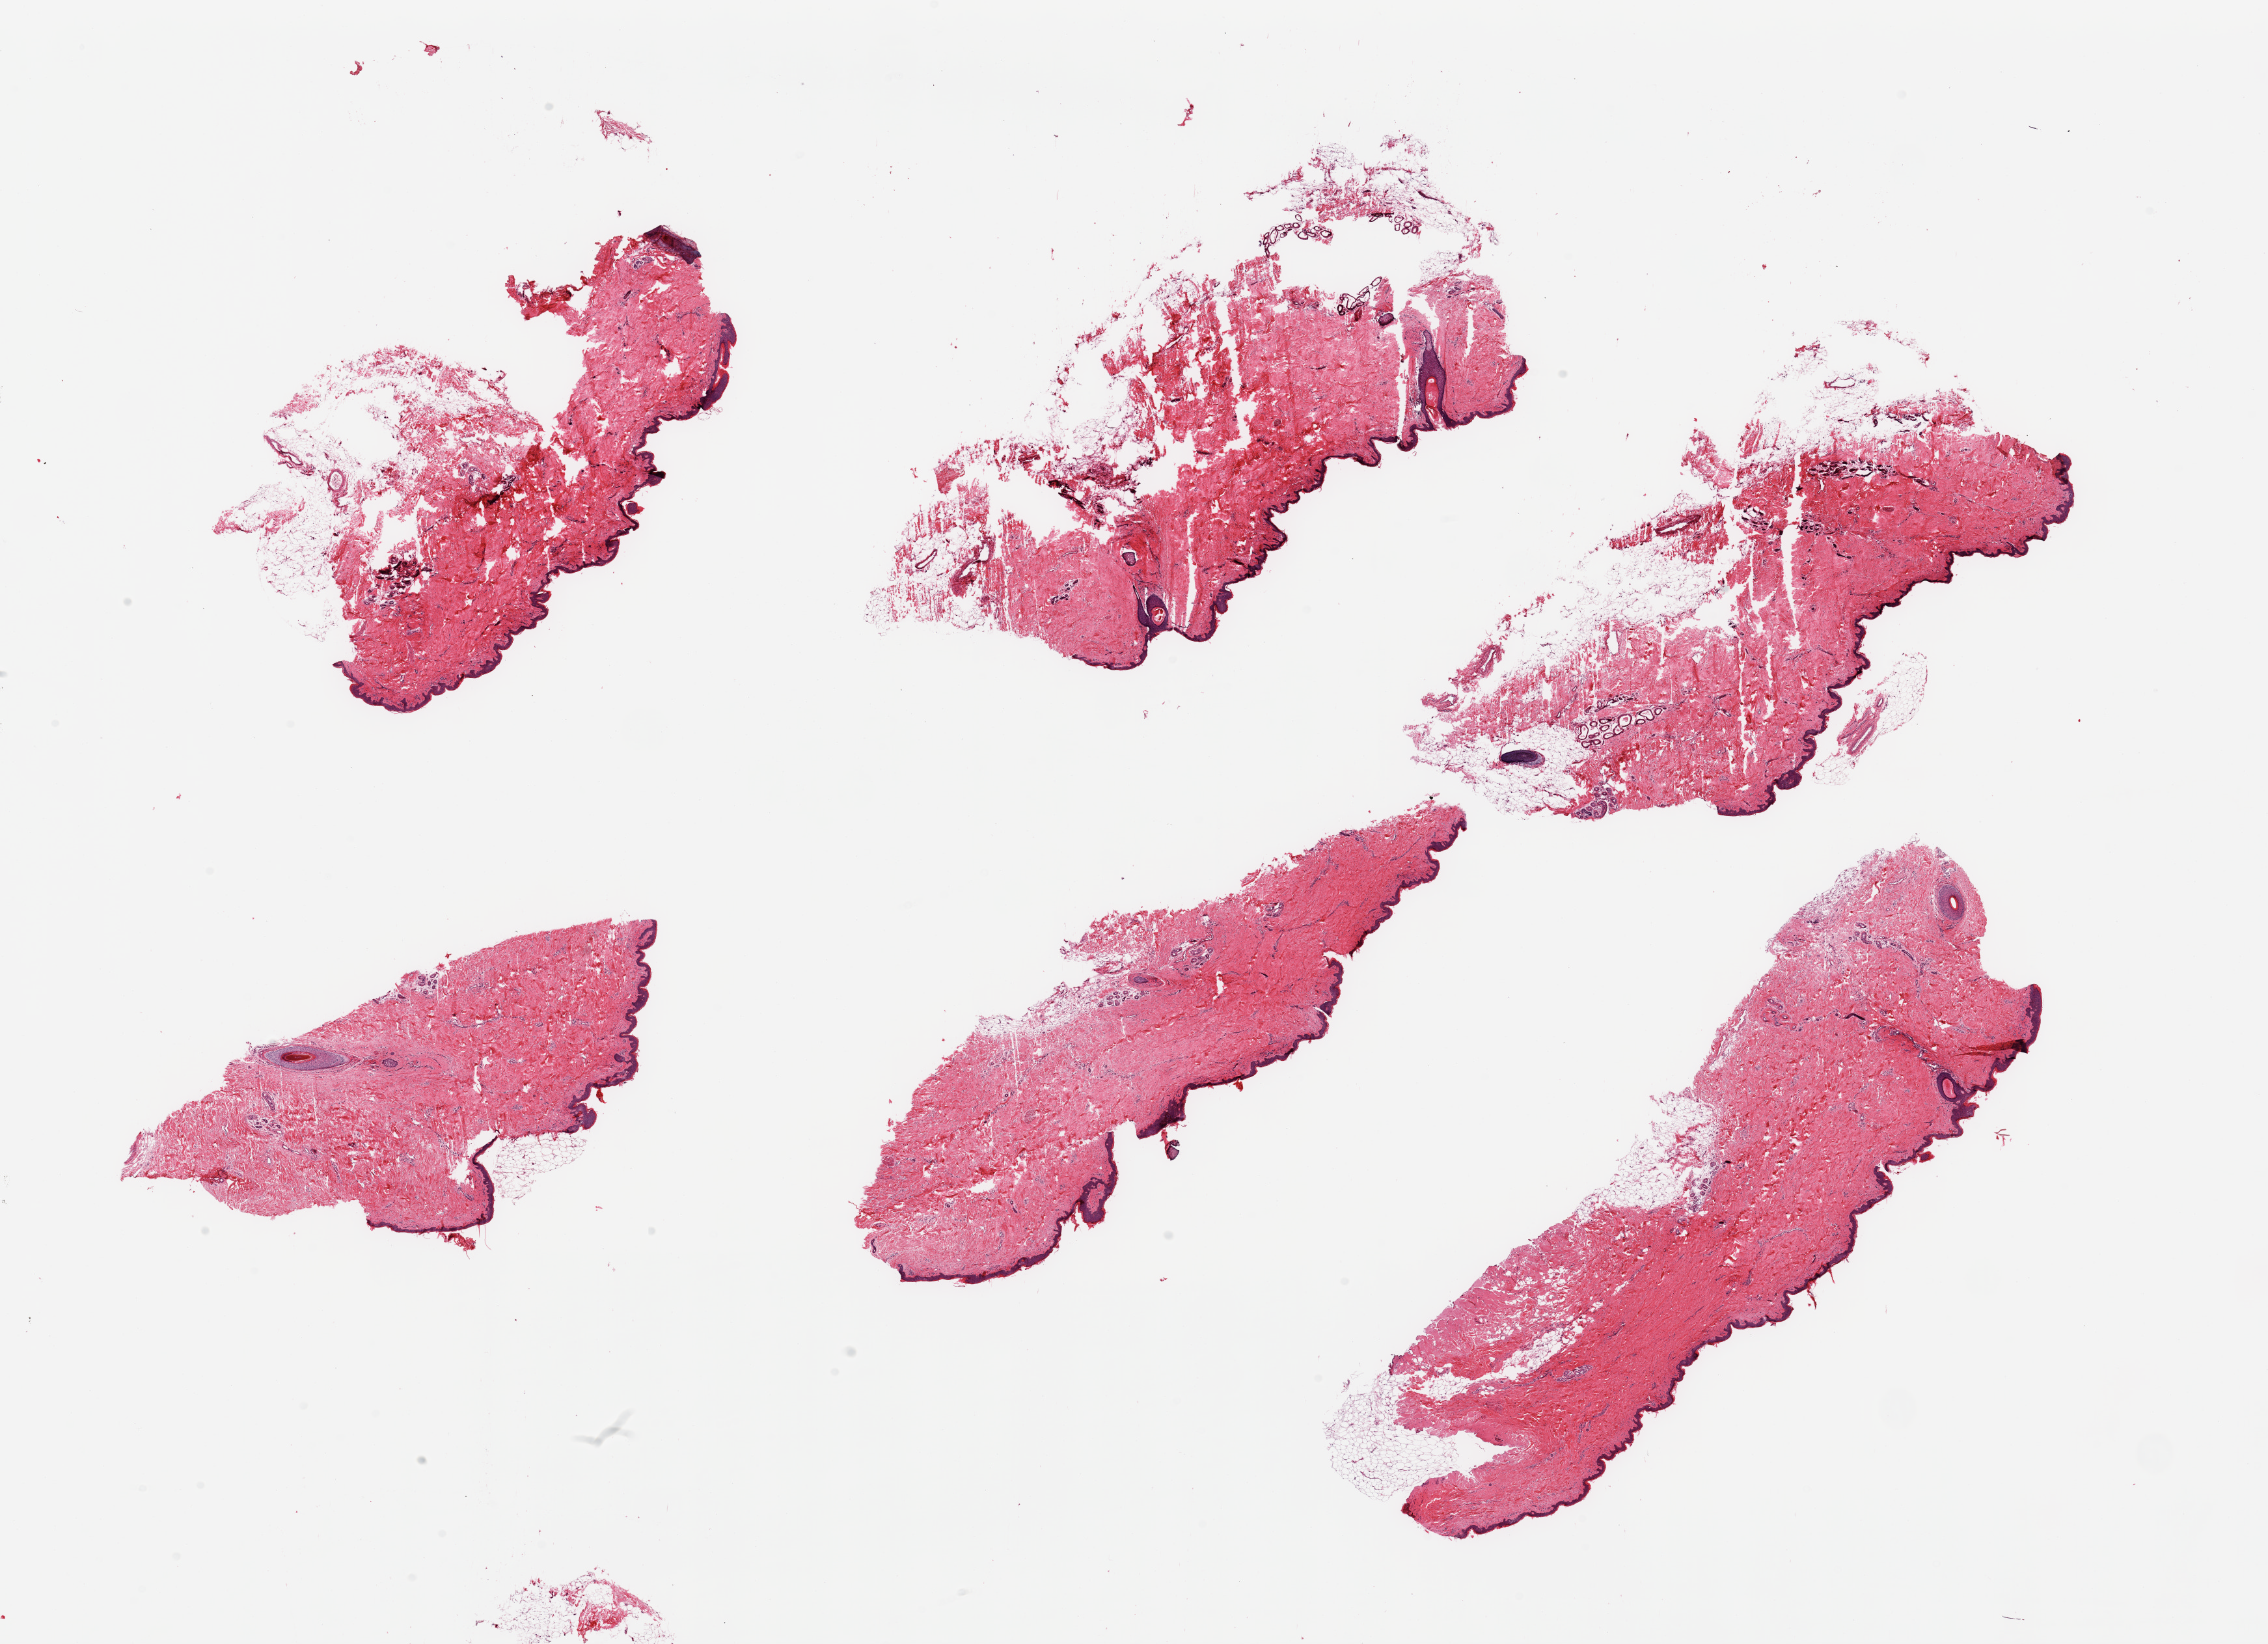
Haematoxylin and eosin whole-slide image — whole scanned area (about 27.6 x 20.0 mm) shown as a low-resolution overview, PAXgene-fixed paraffin-embedded (PFPE) section, target tissue: skin of suprapubic region, donor tissue sample. Donor sex: male.
Pathologist's review note for this sample: 6 pieces; 3 well trimmed, 3 with abundant subcutaneous fat and fragmented.